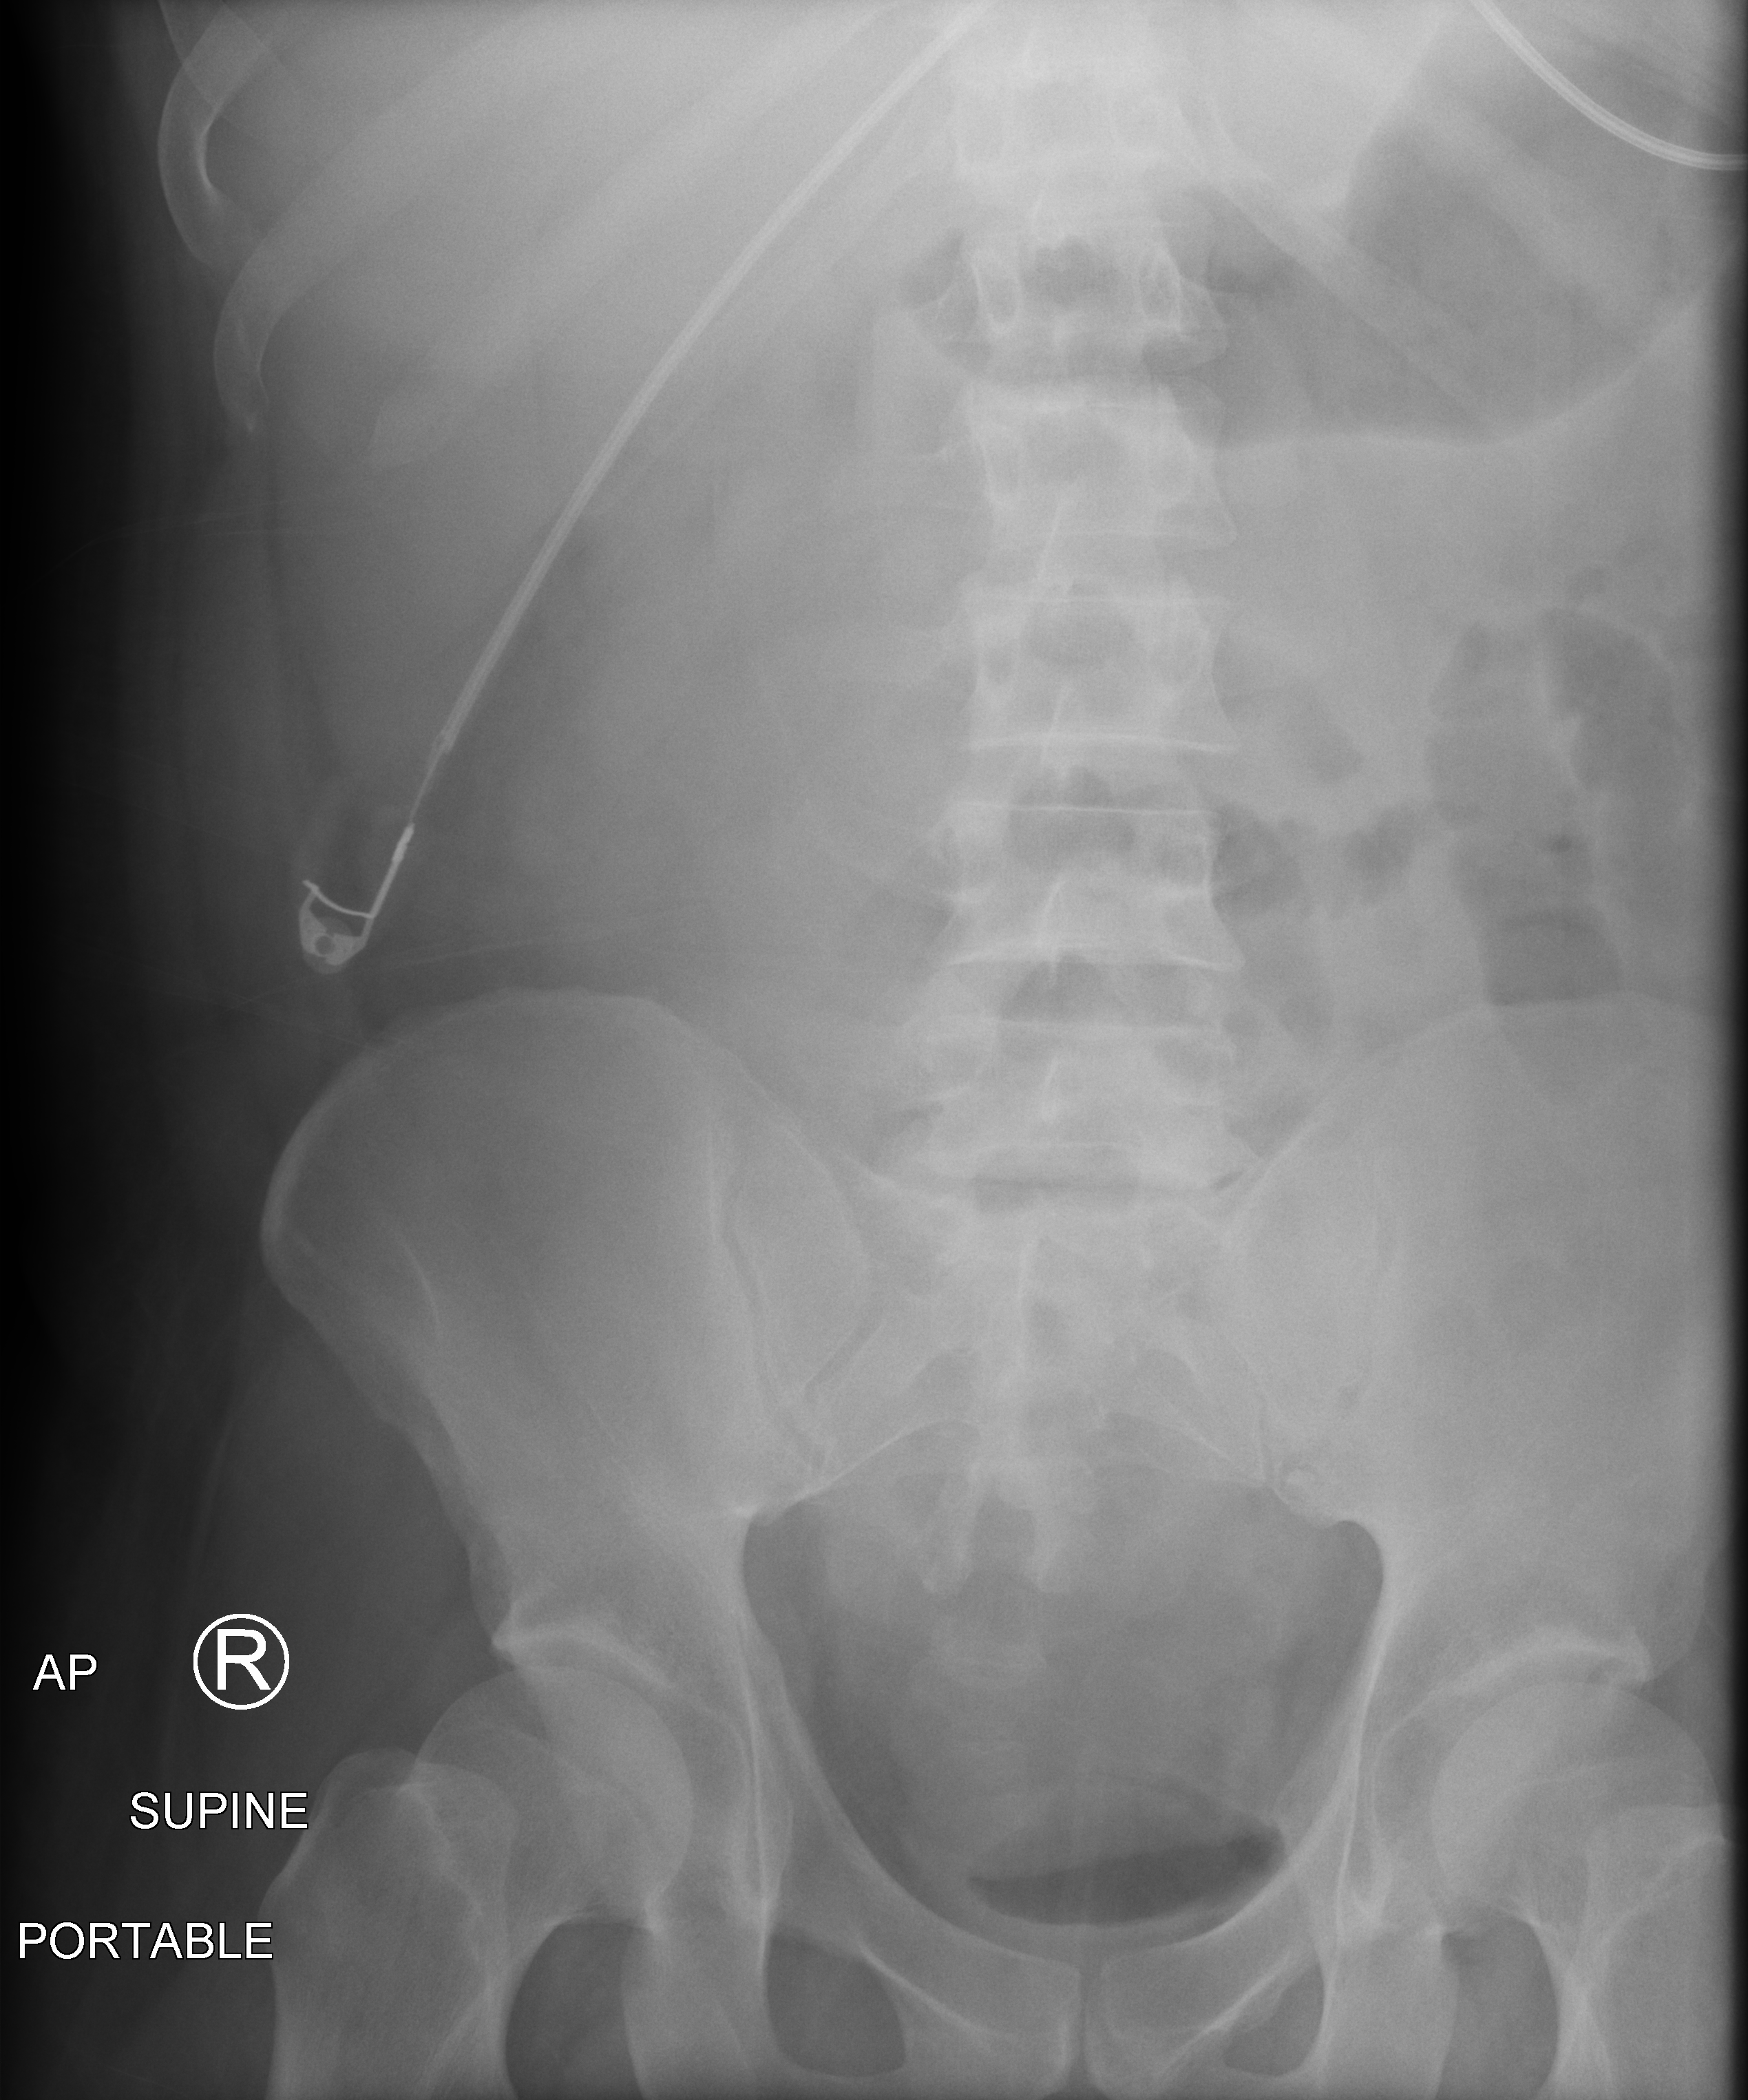
Bedside abdomen radiograph (computed radiography); anteroposterior (AP) projection. Male patient hospitalised with COVID-19, age 18–59 years.
From the hospital-stay record, not from the radiograph (when in the stay this image was taken is not recorded):
- smoking status (admission record): current
- length of hospital stay: 61 days